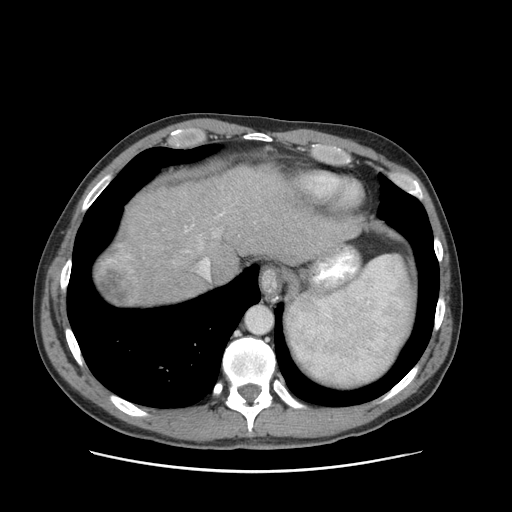
Contrast-enhanced abdominal CT (liver protocol), one axial slice; position 81 of 93 along the scan axis; reconstruction kernel STANDARD; 120 kVp; soft-tissue window (W 400 / L 40 HU); 512 × 512 image matrix. Case-level facts recorded for this patient, not image findings: diagnosis: hepatocellular carcinoma (patient treated with transarterial chemoembolisation; whether this scan precedes or follows treatment is not stated here); TNM stage (as recorded): Stage-II; Child-Pugh class: A; tumour differentiation: moderately differentiated; tumour nodularity: multinodular.
Outlined on this slice (semi-automatic segmentation, software-assisted and operator-edited):
- abdominal aorta: bounding box <245,306,272,333> (left, top, right, bottom; pixels)
- liver parenchyma outside the tumour (the mass and vessels are separate outlines, so this box may not span the whole liver): <104,166,358,304>
- mass: <95,254,139,304>
- liver vessels: <201,259,210,278>